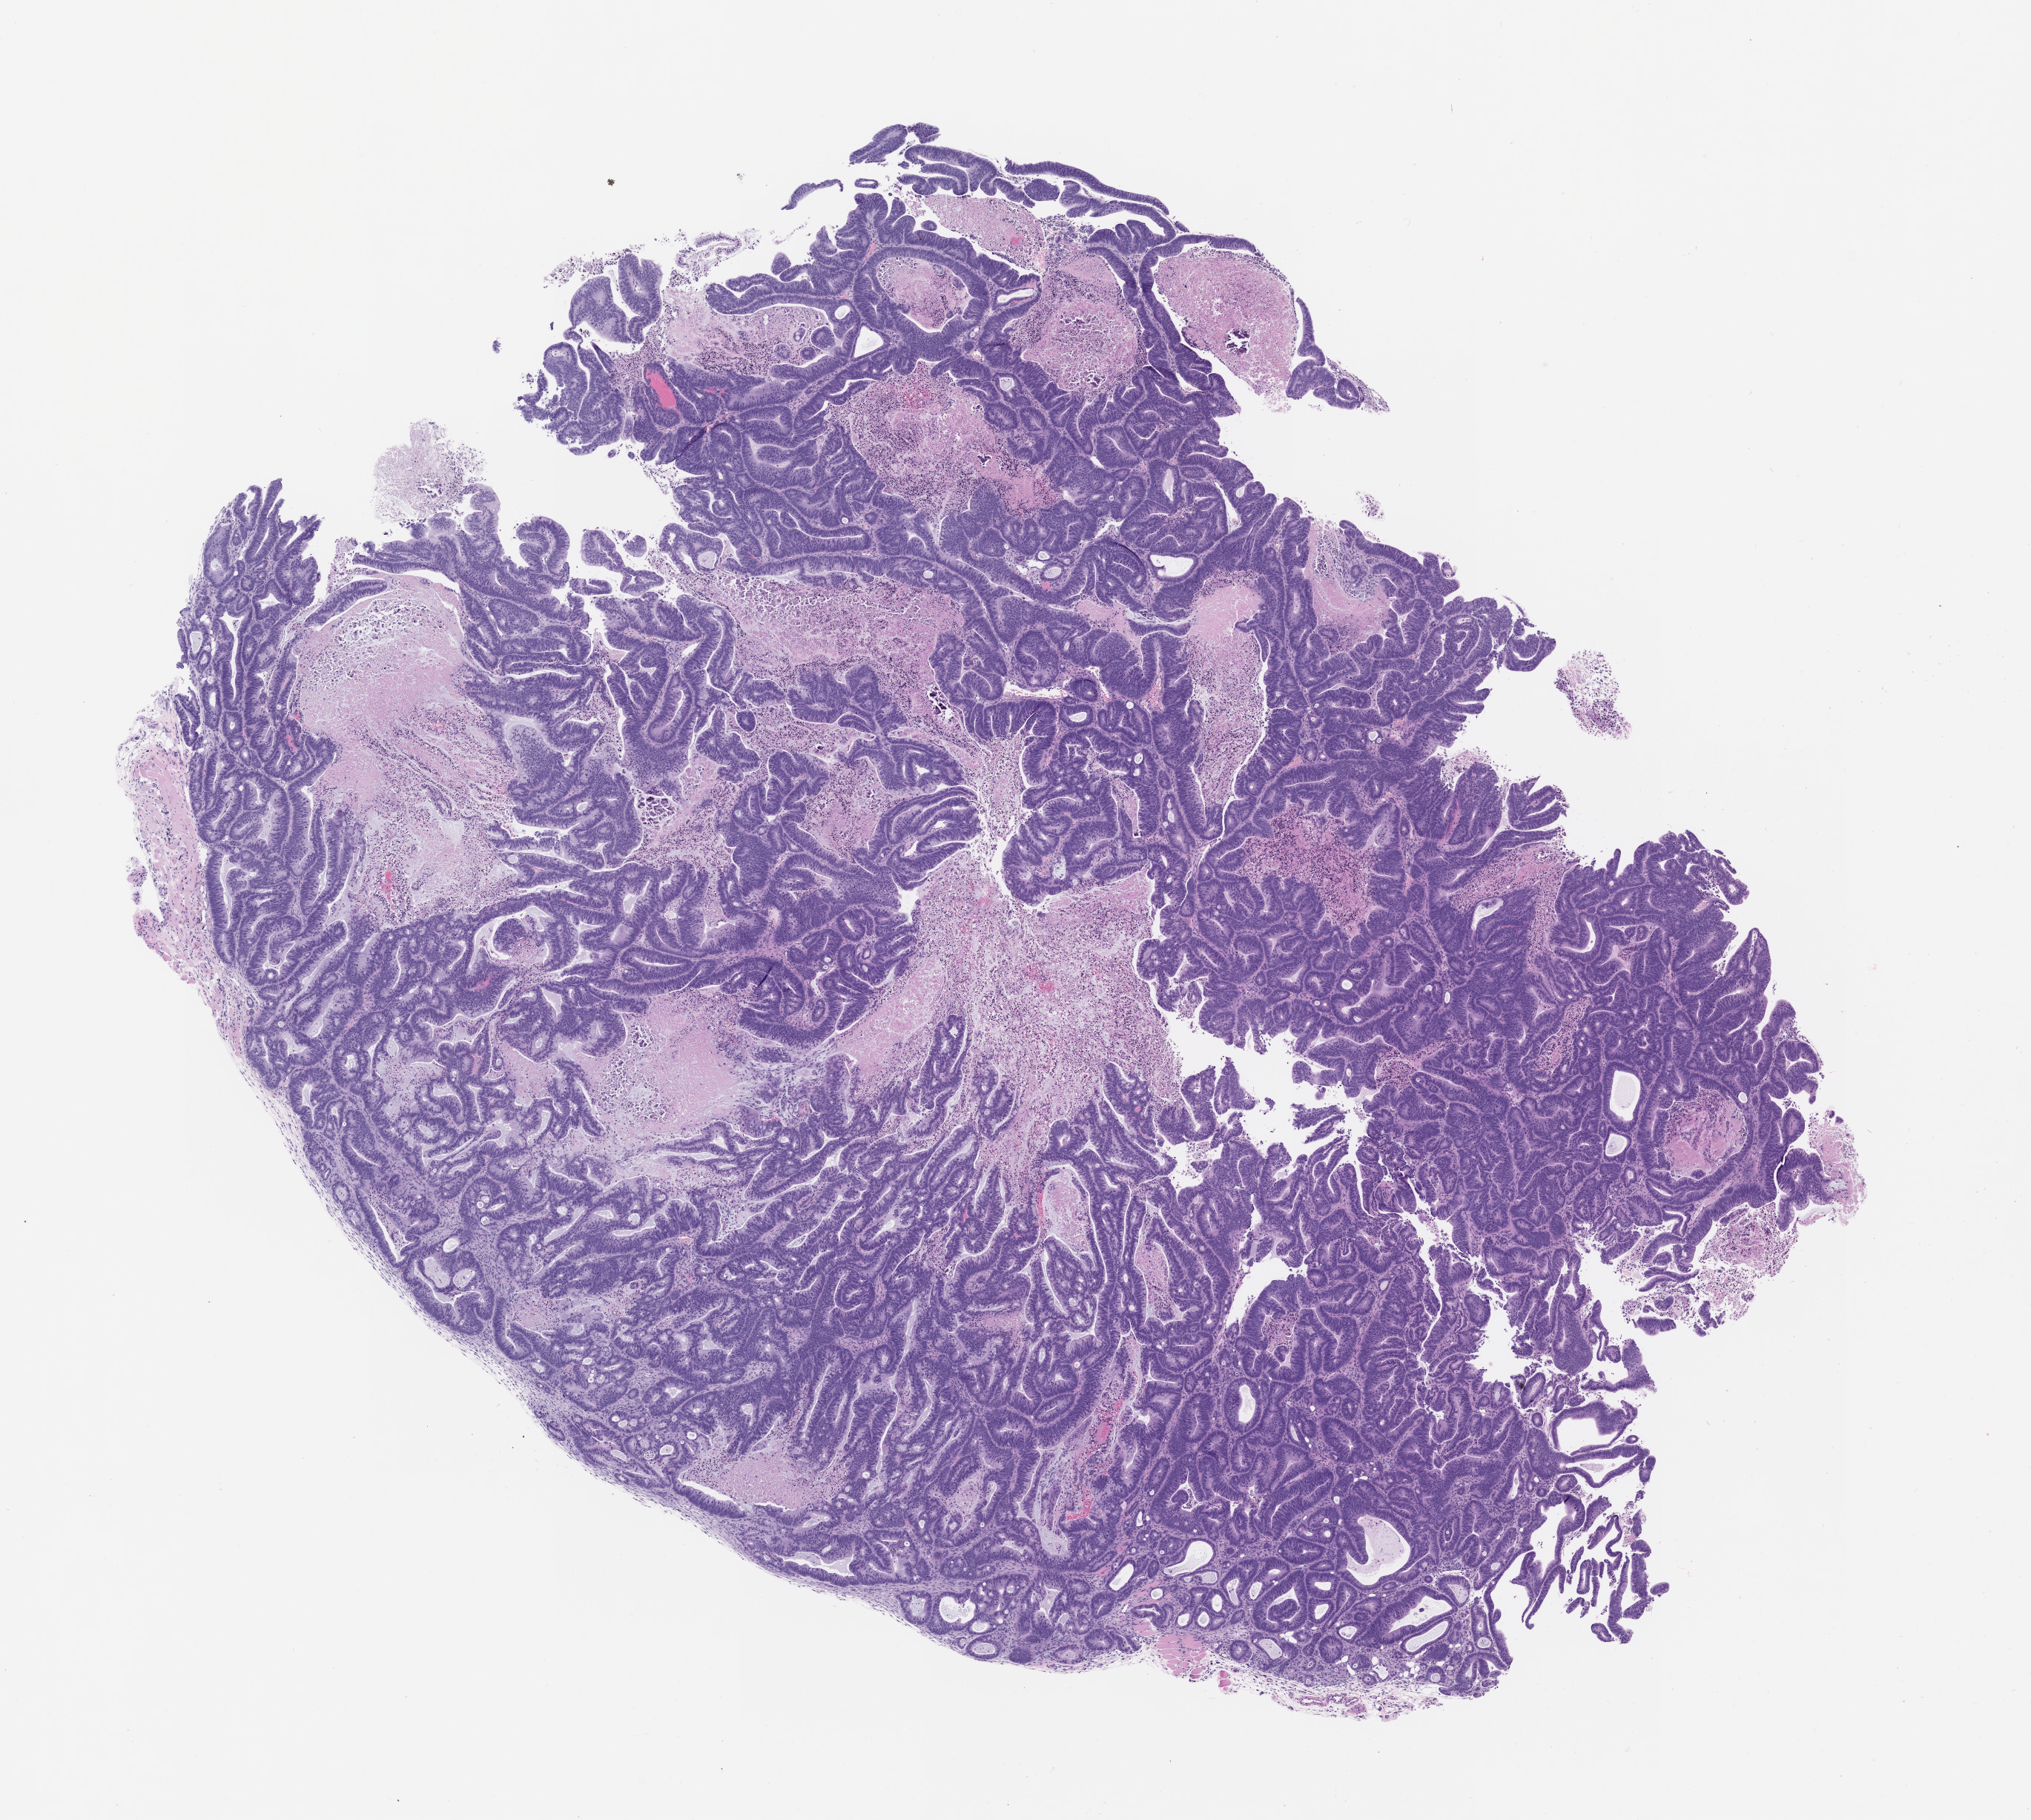
Whole-slide image, hematoxylin and eosin (H&E): patient-derived xenograft (human tumor grown in a mouse), passage 2 — whole scanned area (about 11.0 x 9.9 mm) shown as a low-resolution overview. Formalin-fixed paraffin-embedded section. Tumor site category: colon.
Originating patient diagnosis: Colon Adenocarcinoma.